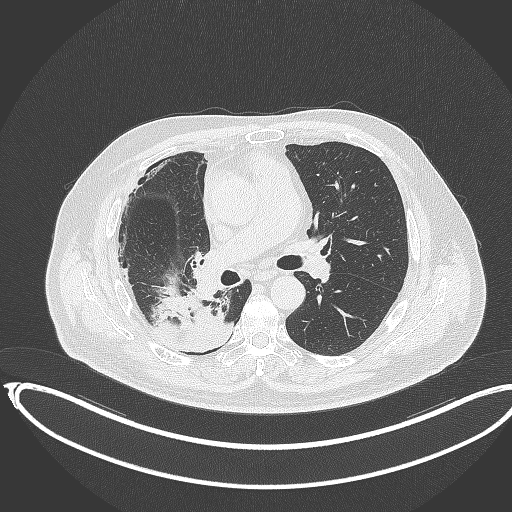
Chest CT, one axial slice; slice 199 of 403 in the series (ordered by position); 120 kVp; lung window (W 1500 / L -600 HU); 512 × 512 image matrix, field of view 436 × 436 mm. Patient: male, 68 years. From the clinical record (not read from this slice): clinical TNM (as recorded): T2a N0 M0.
Outlined on this slice (rectangle marked by the reading radiologist):
- lung tumour (recorded histology: adenocarcinoma): bounding box <142,287,231,355> (left, top, right, bottom; pixels)